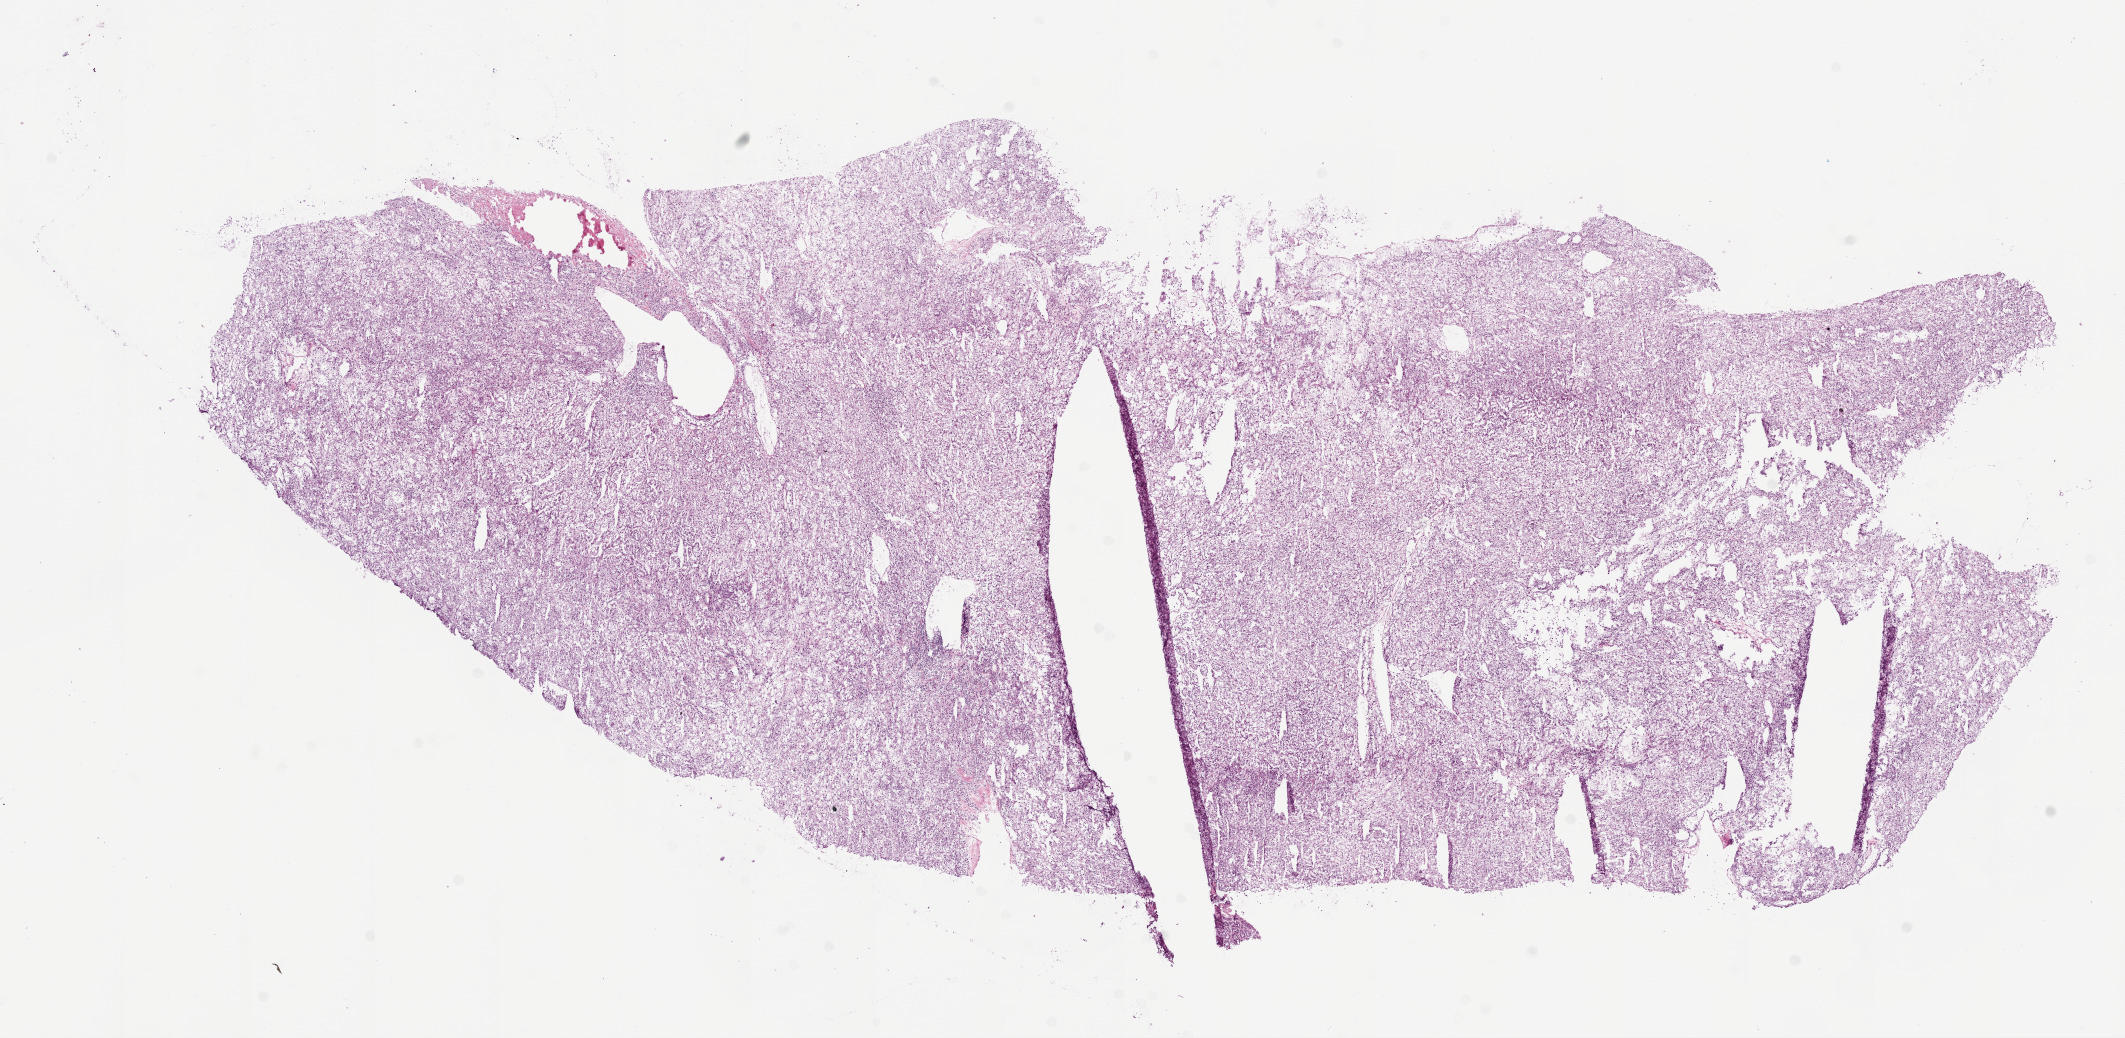
H&E whole-slide image, low-resolution overview of the scanned area, about 17.1 x 8.3 mm (from a 20x scan); frozen section from the top of the tissue portion; primary tumour sample from the kidney. Patient: male, age at initial diagnosis 50 years. Histologic grade: G2 (moderately differentiated). Composition of this section per pathologist review: tumour cells 95%, tumour nuclei 85%, normal cells 0%, stromal cells 5%, necrosis 0%.
AJCC pathologic stage: I (6th edition). Histologic diagnosis: Clear cell adenocarcinoma, NOS. Laterality: right.